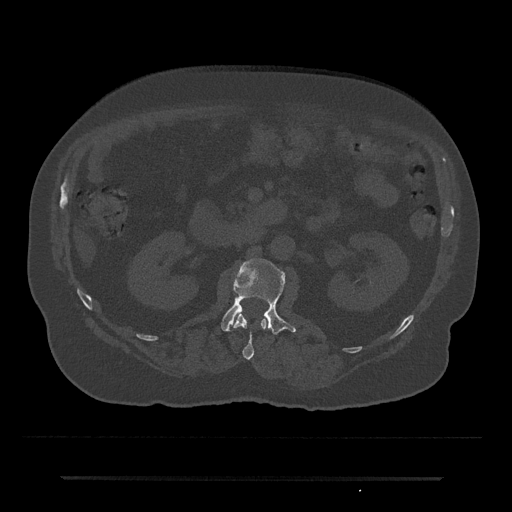
CT including the spine, one axial slice; position 31 of 797 along the scan axis; reconstruction kernel Br40s/3; bone window (W 1800 / L 400 HU); 0.5 mm slice thickness; 512 × 512 image matrix, field of view 437 × 437 mm. Male patient, age 69 years. From the clinical record (not read from this slice): primary cancer: prostate.
Outlined on this slice (semi-automatically segmented with operator editing):
- L1 vertebra: bounding box (x1, y1, x2, y2) in pixels: (234, 314, 267, 360)
- L2 vertebra: (221, 258, 296, 335)